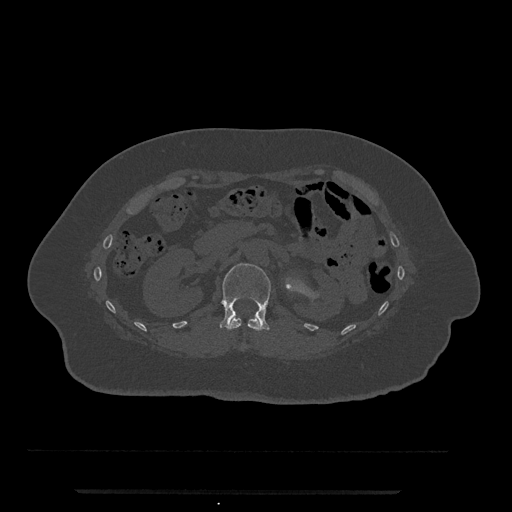
CT including the spine, one axial slice; slice 125 of 797 in the series (ordered by position); reconstruction kernel Br40s/3; bone window (W 1800 / L 400 HU); 0.5 mm slice thickness; 512 × 512 image matrix, field of view 440 × 440 mm. Female patient, age 51 years. Case-level facts recorded for this patient, not image findings: primary cancer: neuro; vertebrae with lytic lesions (as recorded): T8.
Structures marked on this image (semi-automatic segmentation, software-assisted and operator-edited):
- L1 vertebra: bounding box [x1, y1, x2, y2] px = [220, 263, 271, 330]
- T12 vertebra: [227, 317, 263, 348]